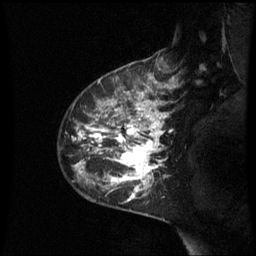
Breast MRI (dynamic contrast-enhanced), one sagittal slice; position 44 of 60 along the scan axis; dynamic contrast-enhanced series, image 2 of 3 at this slice position (ordered by acquisition); 1.5 T; TE 4.2 ms, TR 8.9 ms; 2.4 mm slice thickness; 256 × 256 image matrix. Patient: female, 42 years. From the clinical record (not read from this slice): setting: breast cancer imaged before/during neoadjuvant chemotherapy; receptor status: HER2-positive.
Structures marked on this image (semi-automatically segmented with operator editing):
- analysis volume of interest (the breast-tissue region the enhancement analysis was run in; not a lesion): bounding box (x1, y1, x2, y2) in pixels: (63, 93, 171, 210)
- tumour enhancement mask (voxels above the 70 % enhancement threshold inside the analysis volume of interest): (76, 93, 170, 201)